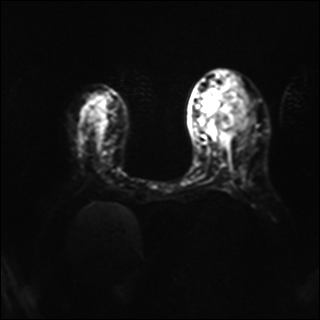
Breast MRI, one axial slice. Position 19 of 40 along the scan axis. Diffusion-weighted series; image 2 of 4 stored at this slice position (different b-values; order by instance number). 1.5 T. 320 × 320 image matrix, field of view 320 × 320 mm. Female patient.
Outlined on this slice (expert manual segmentation):
- tumour on diffusion-weighted imaging: bounding box [x1, y1, x2, y2] px = [216, 95, 246, 131]